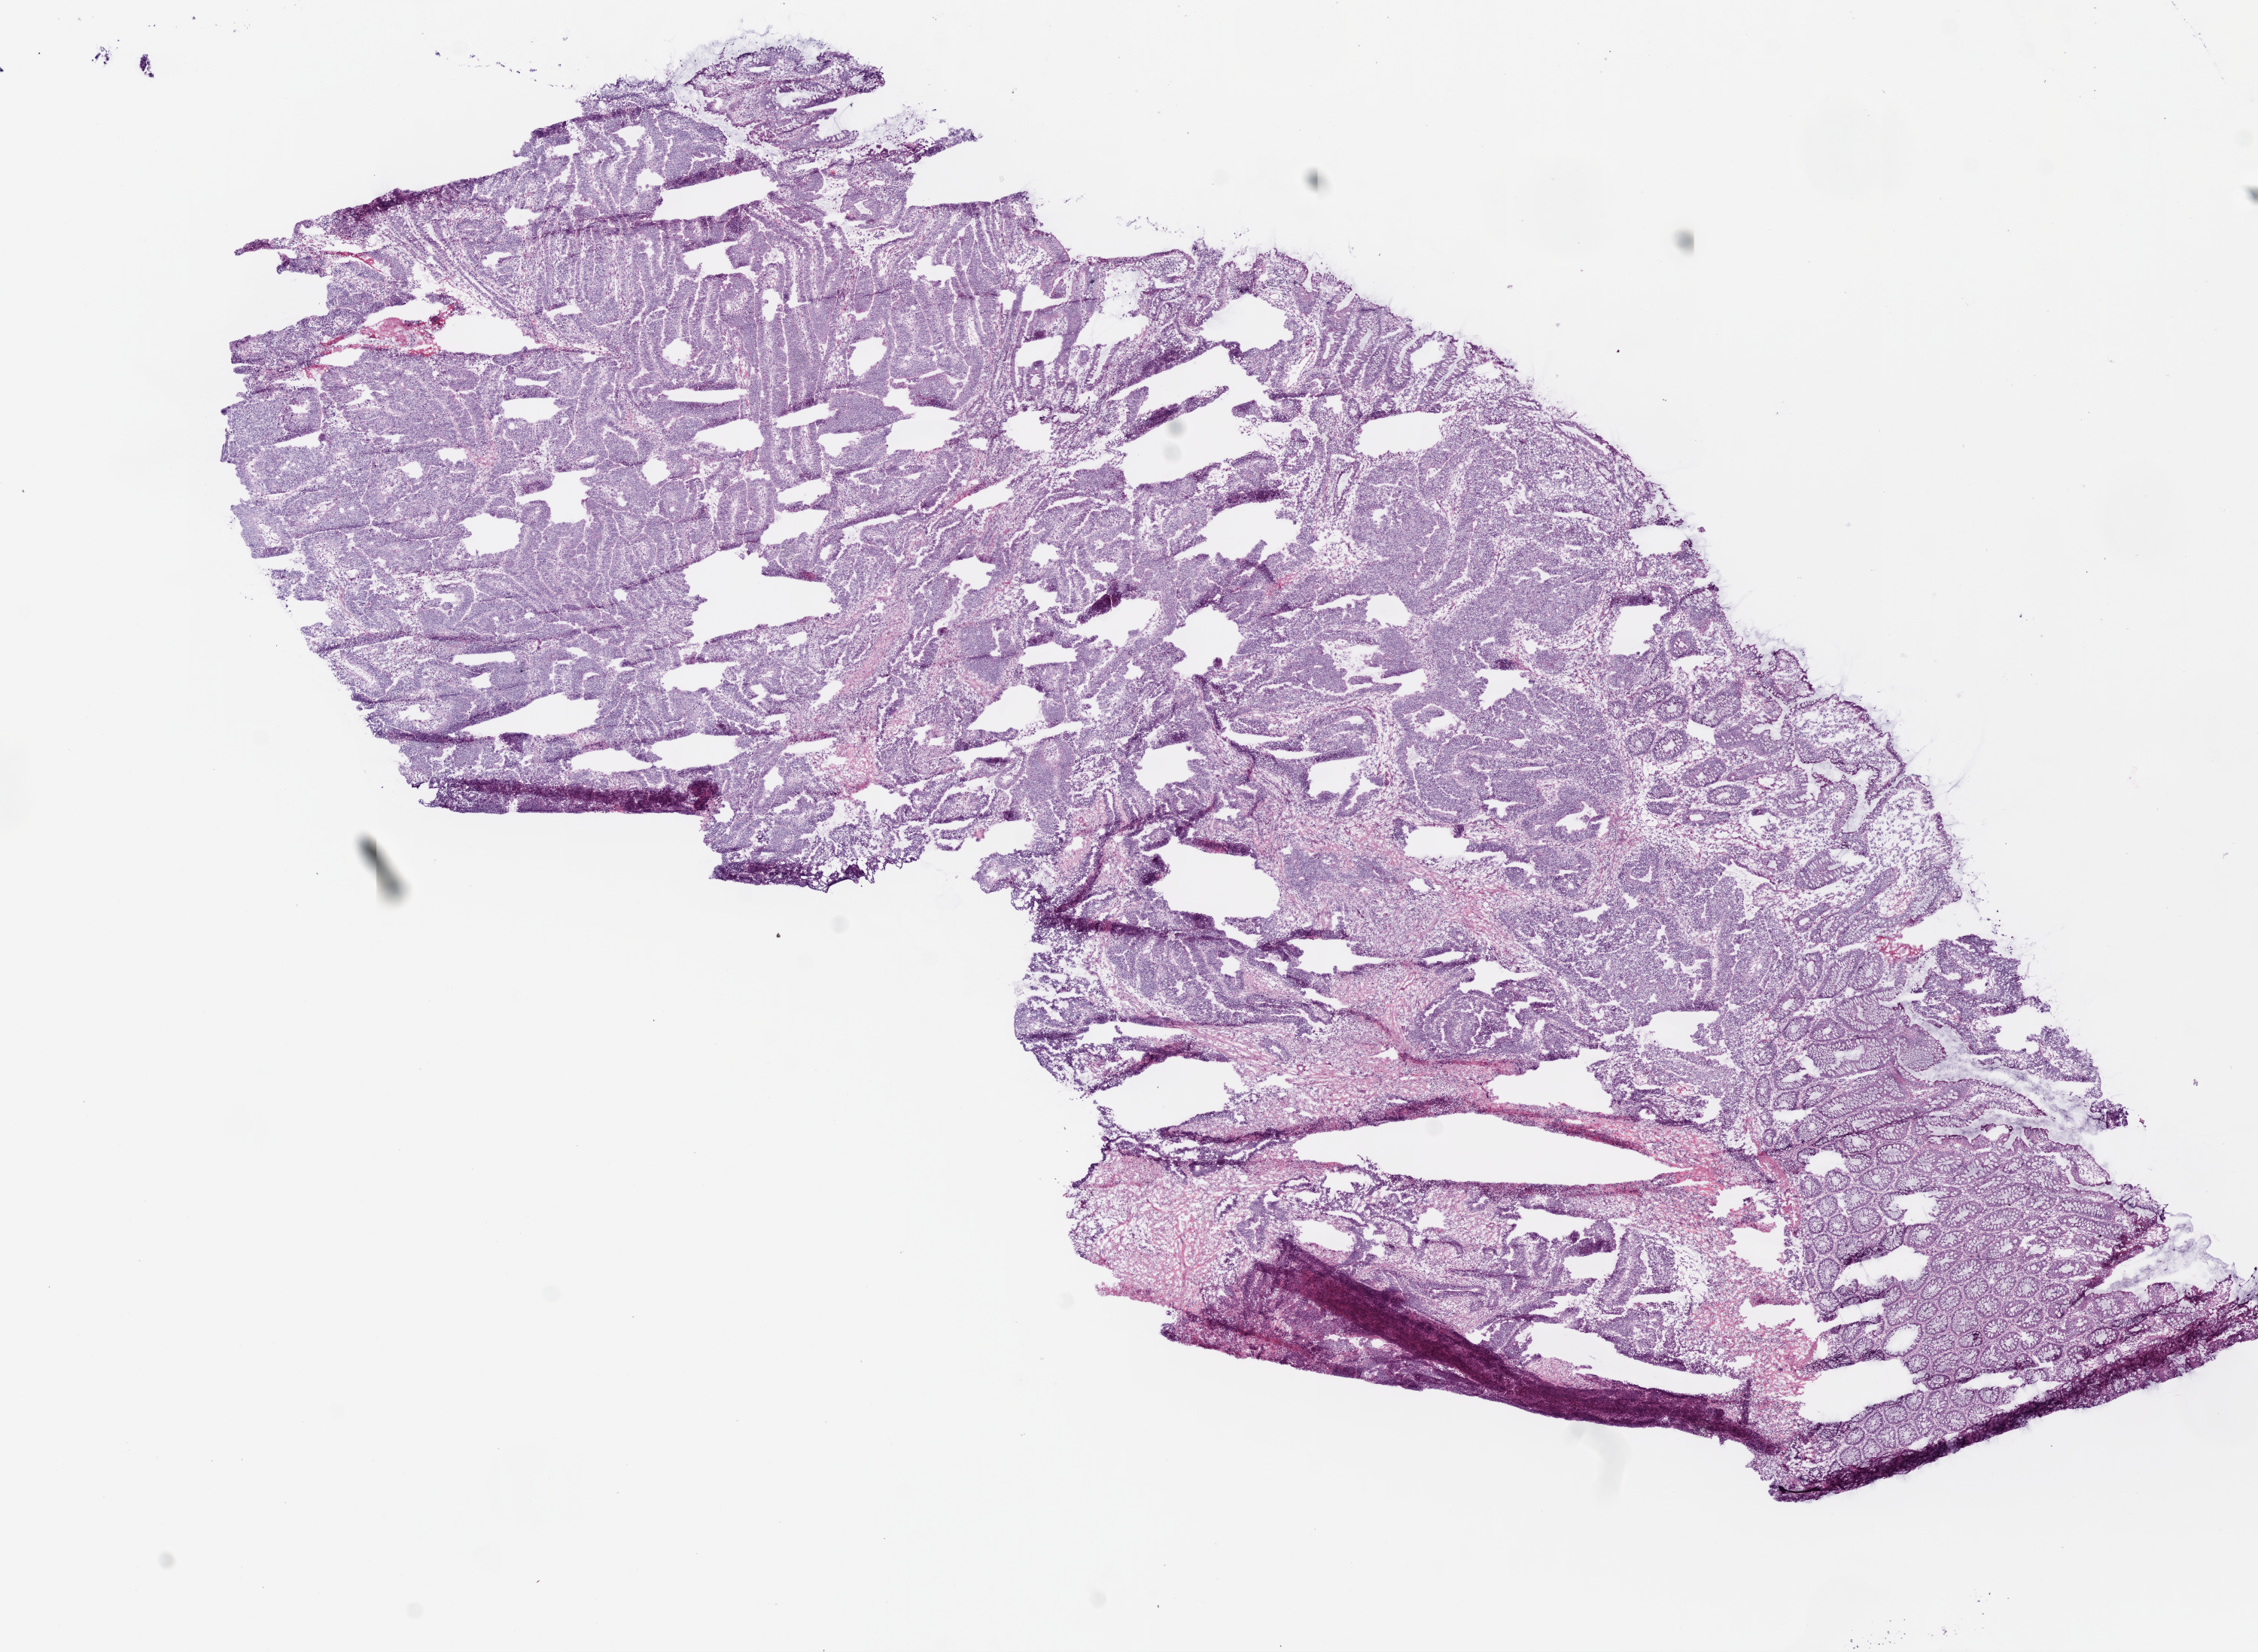
H&E whole-slide image — whole scanned area (about 12.0 x 8.8 mm) shown as a low-resolution overview; frozen section; rectum, primary tumour sample. Male, age 62 years at initial diagnosis. Slide review estimates, as recorded: tumour cells 85%, tumour nuclei 85%, normal cells 10%, stromal cells 5%, necrosis 0%.
* TNM: T3 N2 M0
* AJCC pathologic stage: IIIC (6th edition)
* diagnosis: Adenocarcinoma, NOS (rectosigmoid junction)
* lymph nodes positive (case pathology): 31 of 45 examined